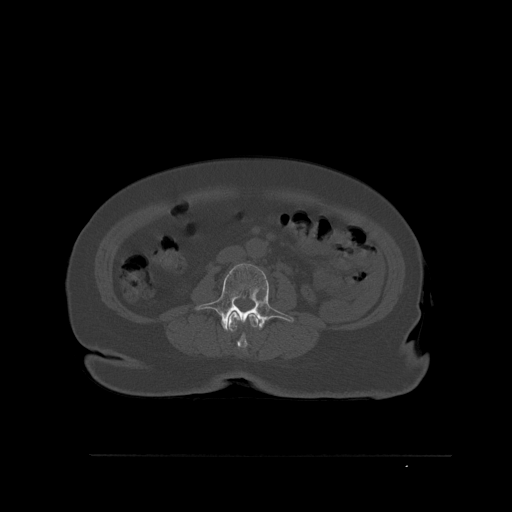
CT including the spine, one axial slice. Position 229 of 527 along the scan axis. Bone window (W 1800 / L 400 HU). 1.5 mm slice thickness. 512 × 512 image matrix, field of view 470 × 470 mm. Female patient, age 73 years. Case-level facts recorded for this patient, not image findings: primary cancer: breast.
Outlined on this slice (semi-automatic segmentation, software-assisted and operator-edited):
- L2 vertebra: bounding box [x1, y1, x2, y2] px = [228, 312, 259, 352]
- L3 vertebra: [195, 263, 294, 332]